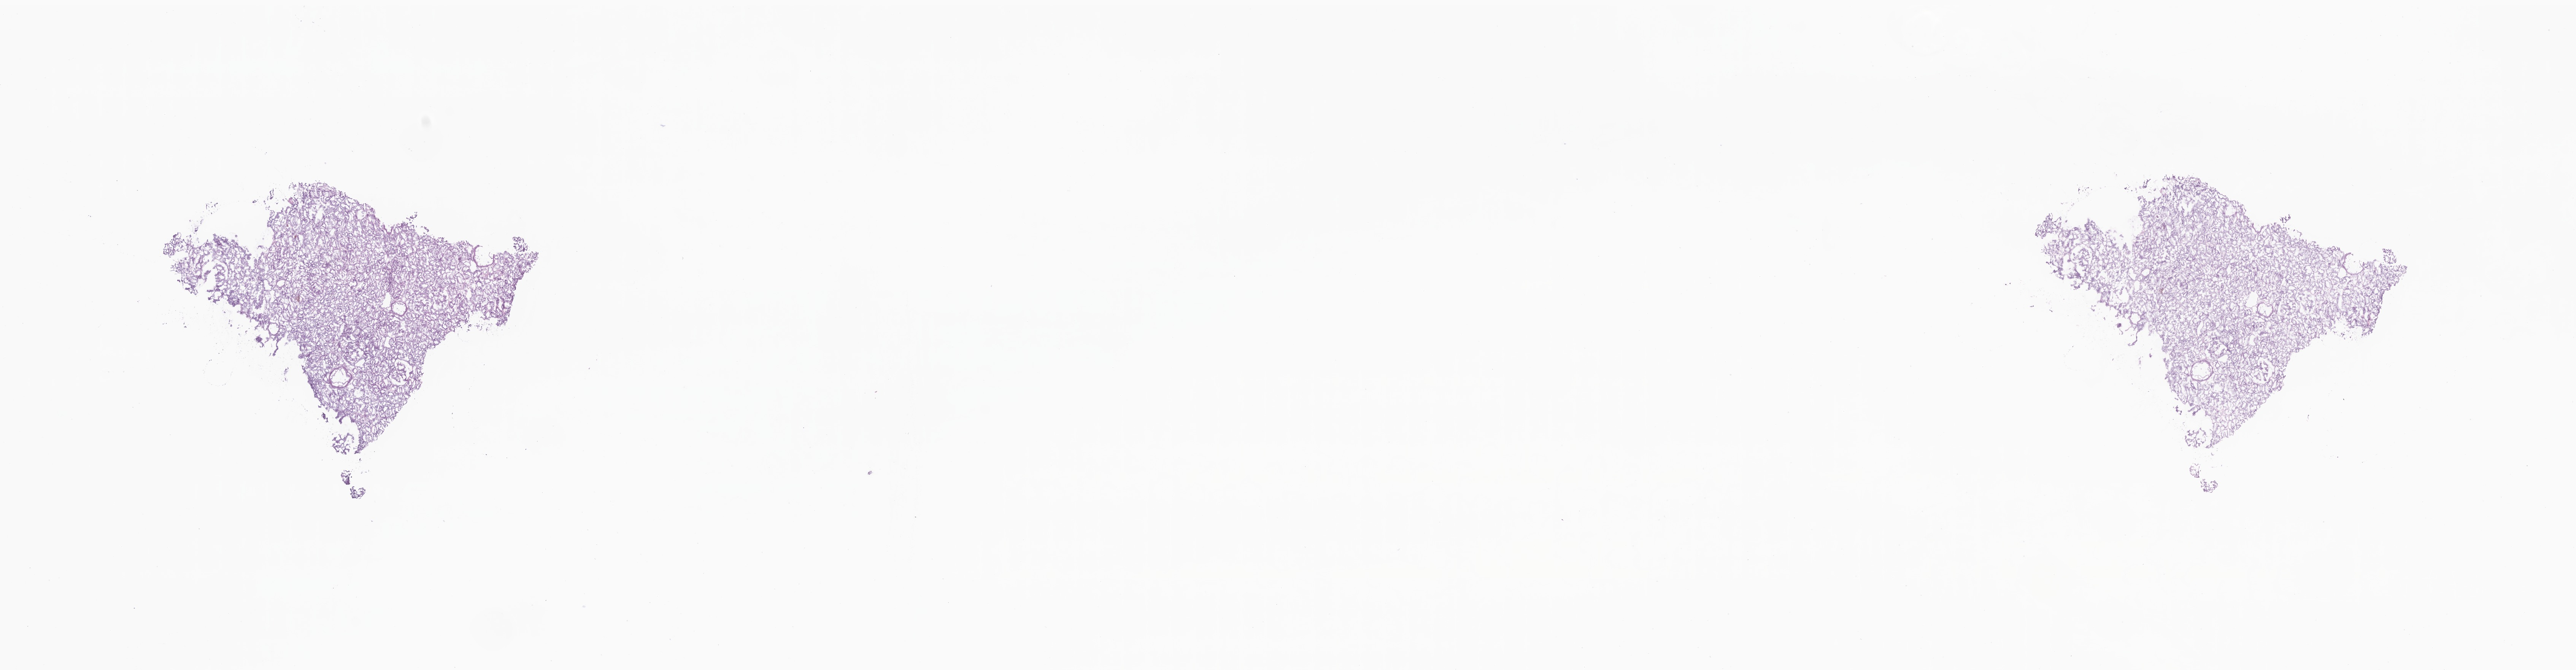
Haematoxylin and eosin whole-slide image, whole scanned area (about 28.6 x 7.4 mm) shown as a low-resolution overview. Frozen section (tissue freezing medium). Non-tumor (normal tissue) sample from a patient with clear cell adenocarcinoma, NOS. Site: kidney. Male patient; age at initial diagnosis 50 years. Composition of this section per pathologist review: tumor cells 0%, tumor nuclei 0%, stromal cells 15%, necrosis 0%, normal cells 85%. Inflammatory infiltration, as recorded: lymphocyte infiltration 0%, monocyte infiltration 0%, neutrophil infiltration 0%.
This section: non-tumor tissue sample; the patient's diagnosis is given above.